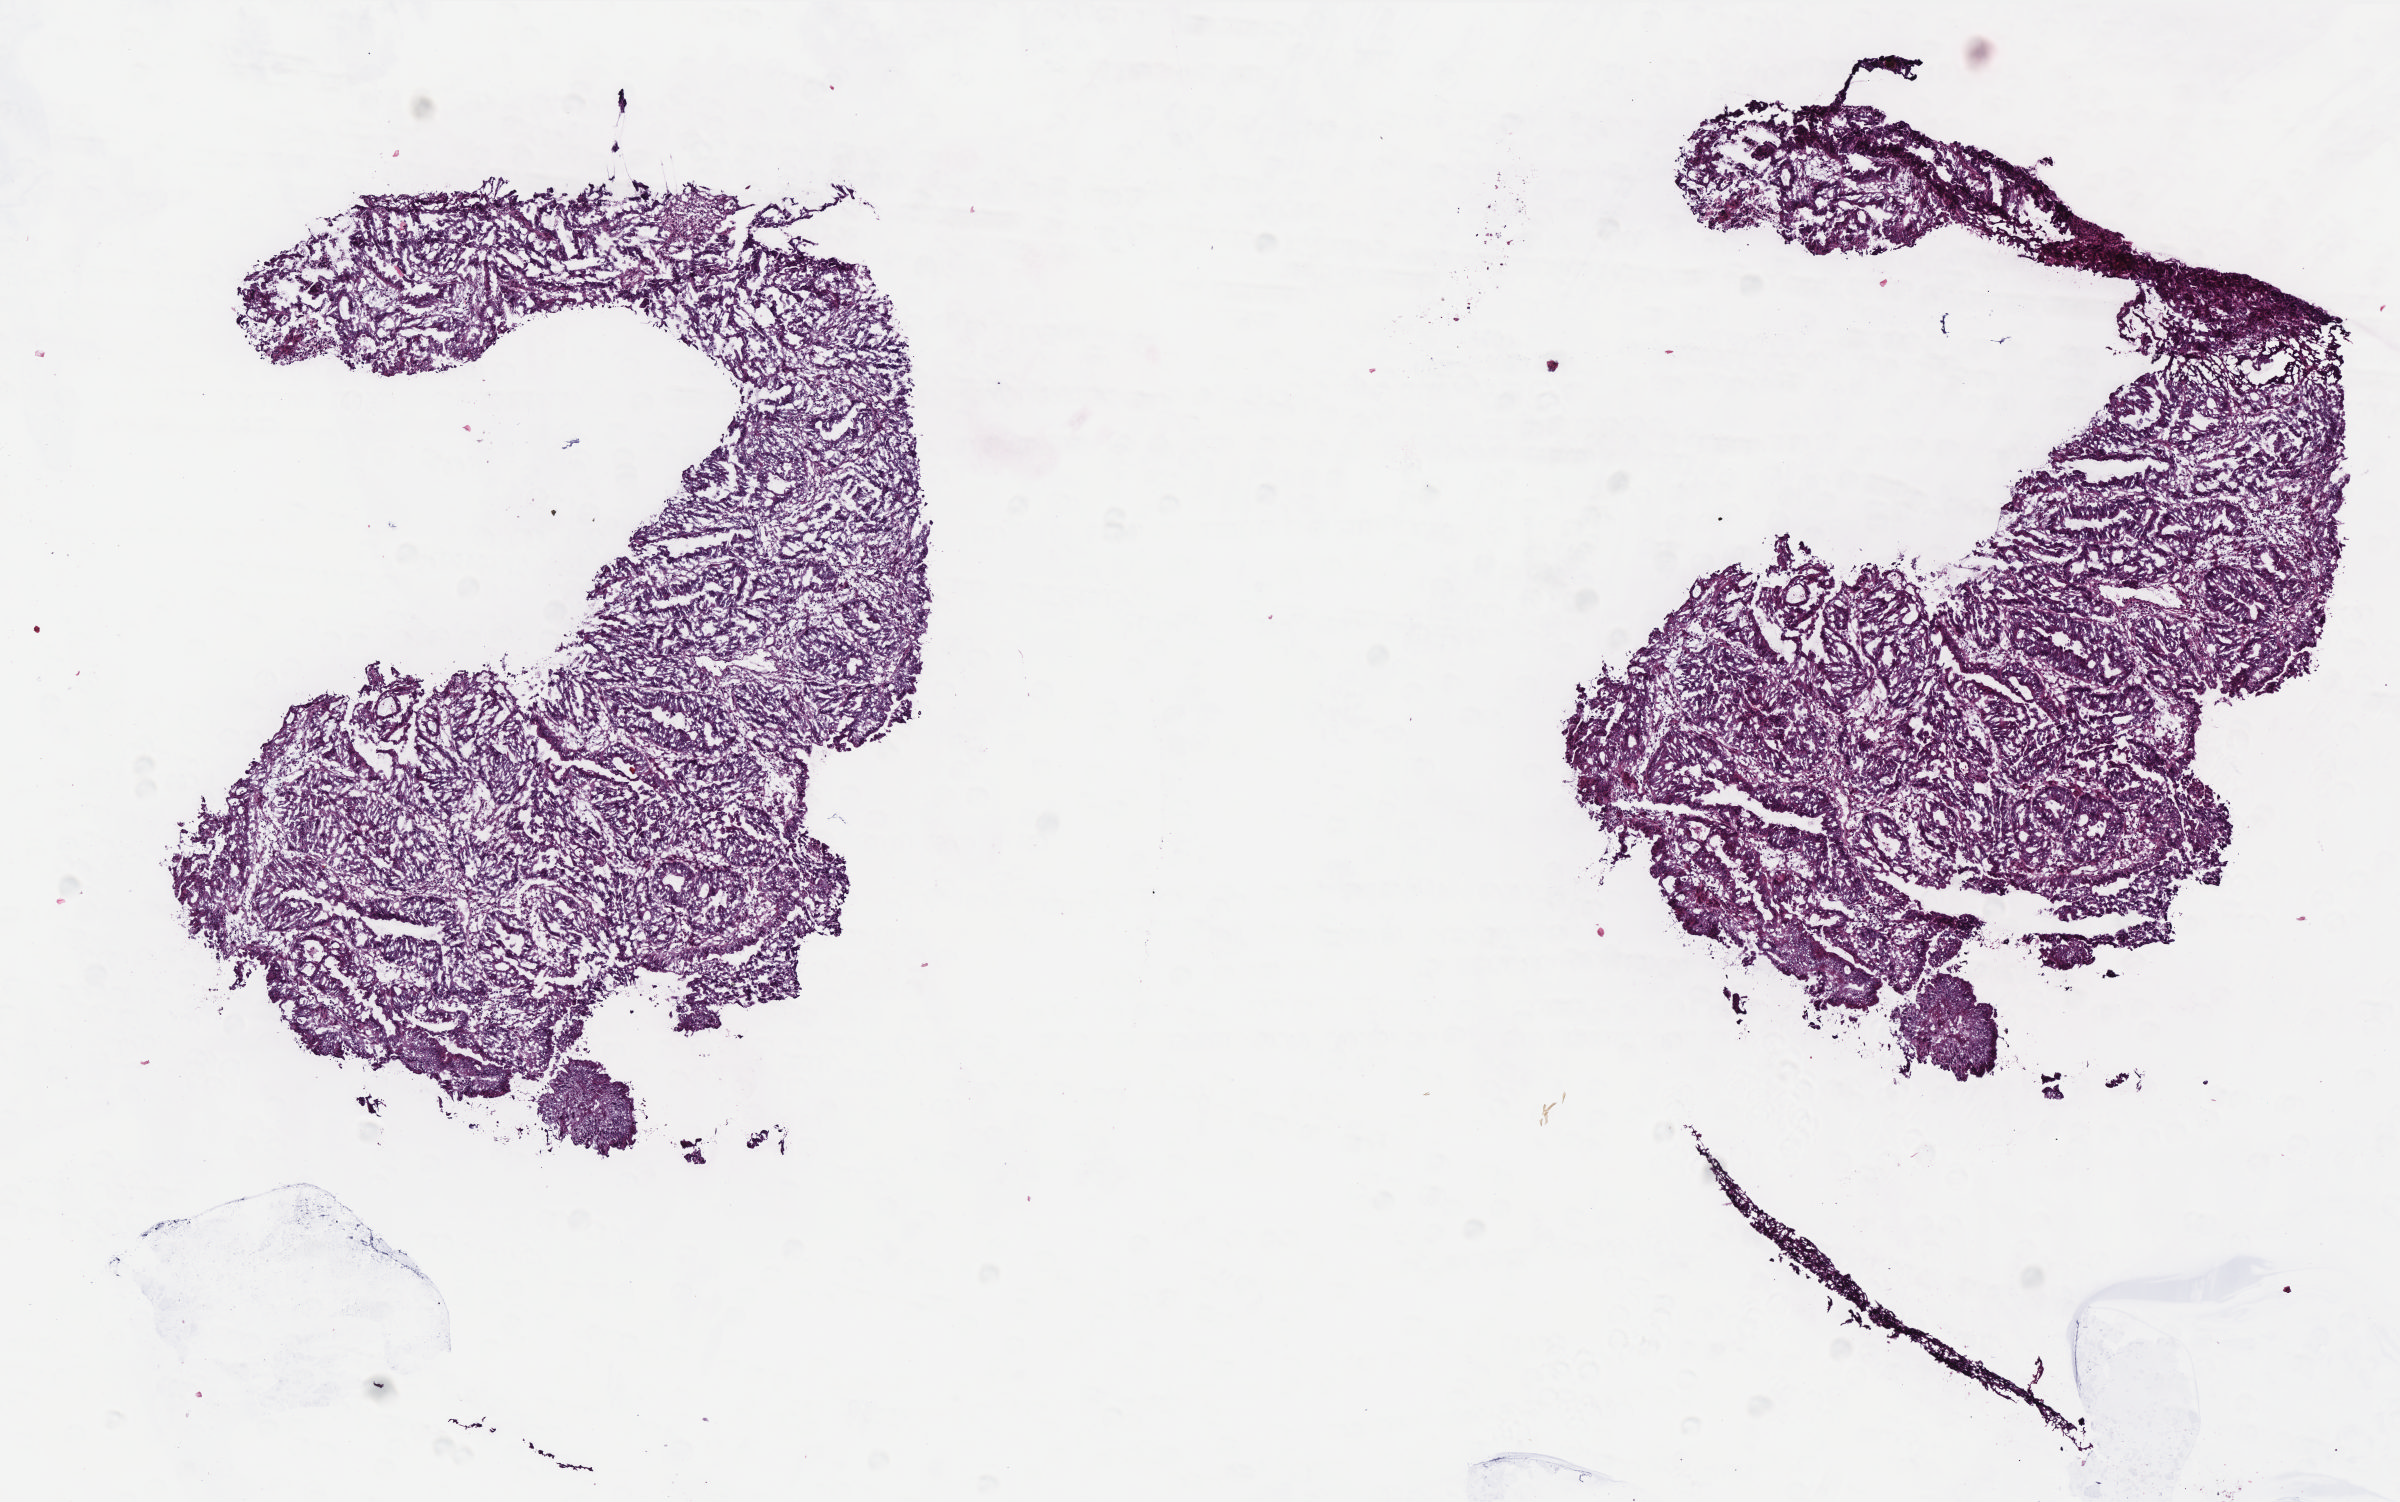
Whole-slide histology image, H&E-stained — whole scanned area (about 9.6 x 6.0 mm) shown as a low-resolution overview; frozen section; primary tumour sample from the rectum. Female, age 68 years at initial diagnosis. Composition of this section per pathologist review: tumour cells 95%, tumour nuclei 90%.
Diagnosis: Adenocarcinoma, NOS.